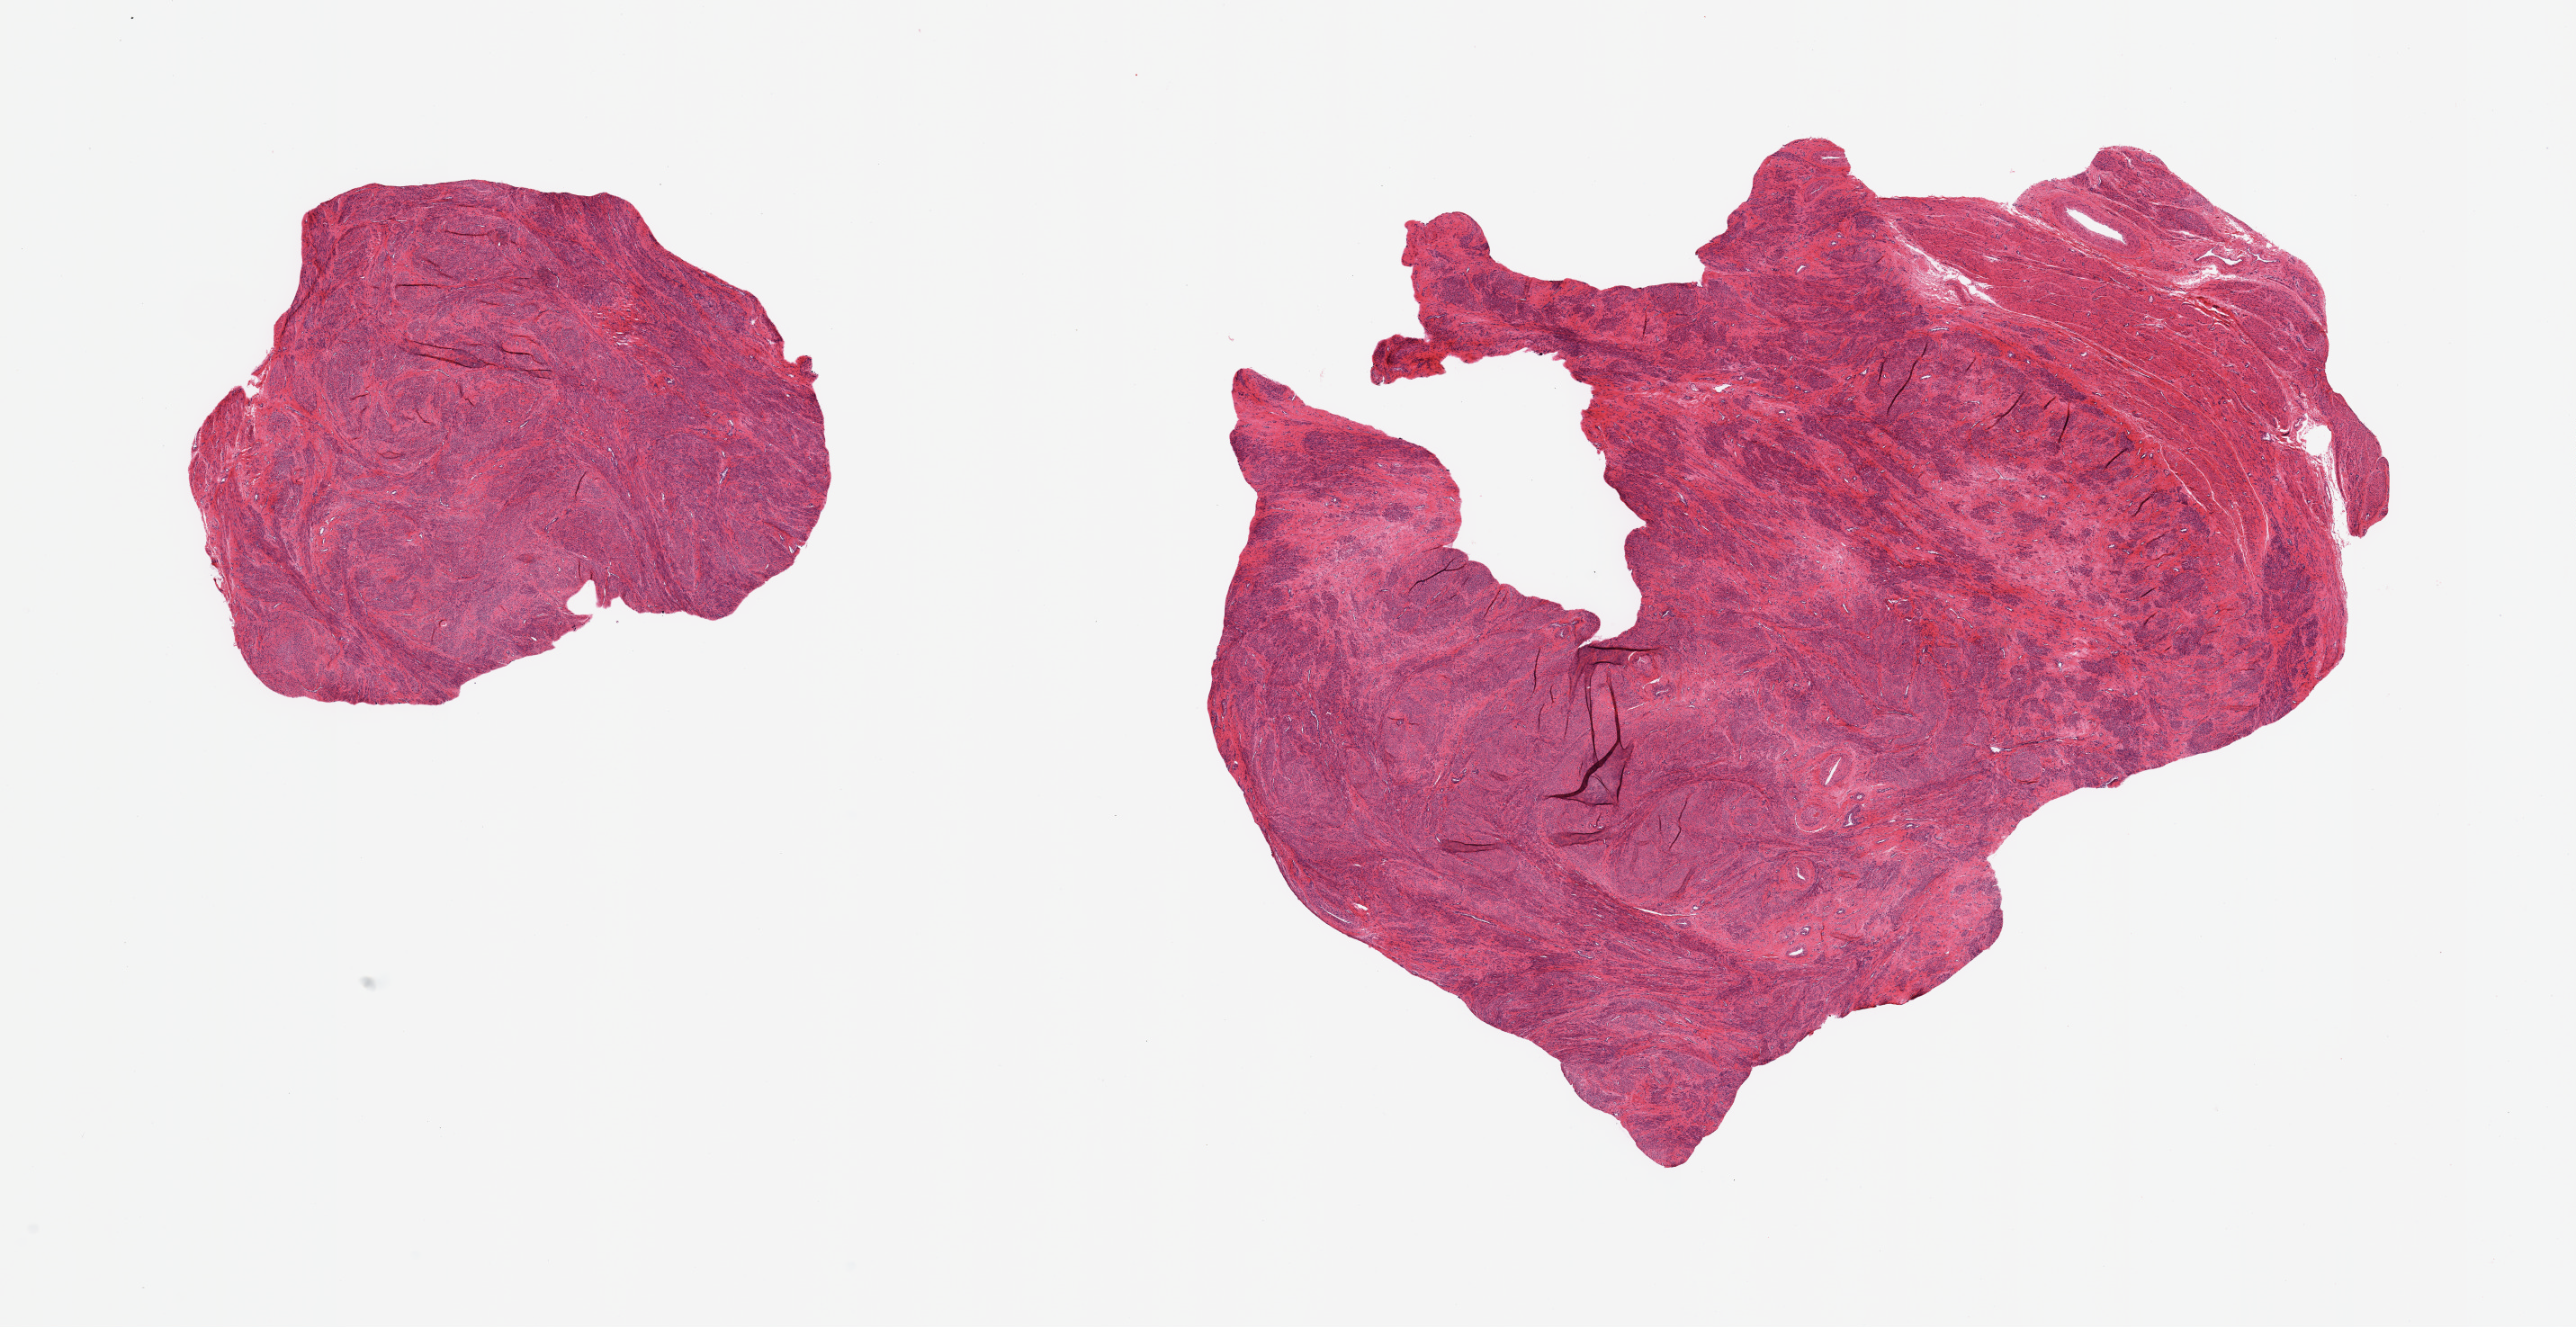
Whole-slide image, hematoxylin and eosin (H&E) stain, whole scanned area (about 22.6 x 11.7 mm) shown as a low-resolution overview, PAXgene-fixed, paraffin-embedded tissue, sampled site (target tissue): uterus, tissue donor sample. Female donor.
Review note (as recorded): 2 pieces myometrium; features of leiomyoma.